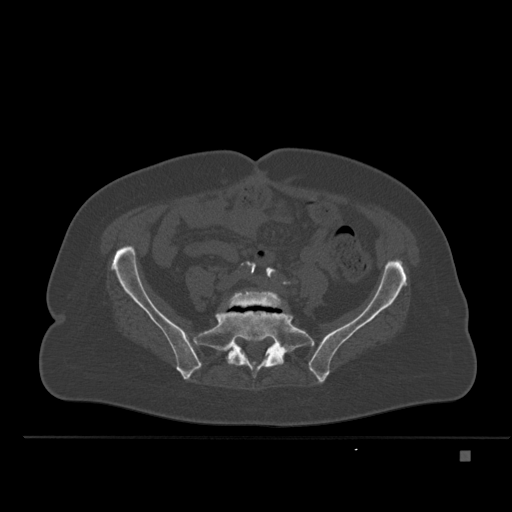
CT including the spine, one axial slice. Position 149 of 477 along the scan axis. Bone window (W 1800 / L 400 HU). 1.5 mm slice thickness. 512 × 512 image matrix. Female patient, age 74 years. Case-level facts recorded for this patient, not image findings: primary cancer: colon.
Structures marked on this image (semi-automatic segmentation, software-assisted and operator-edited):
- L5 vertebra: bounding box <228,291,283,308> (left, top, right, bottom; pixels)